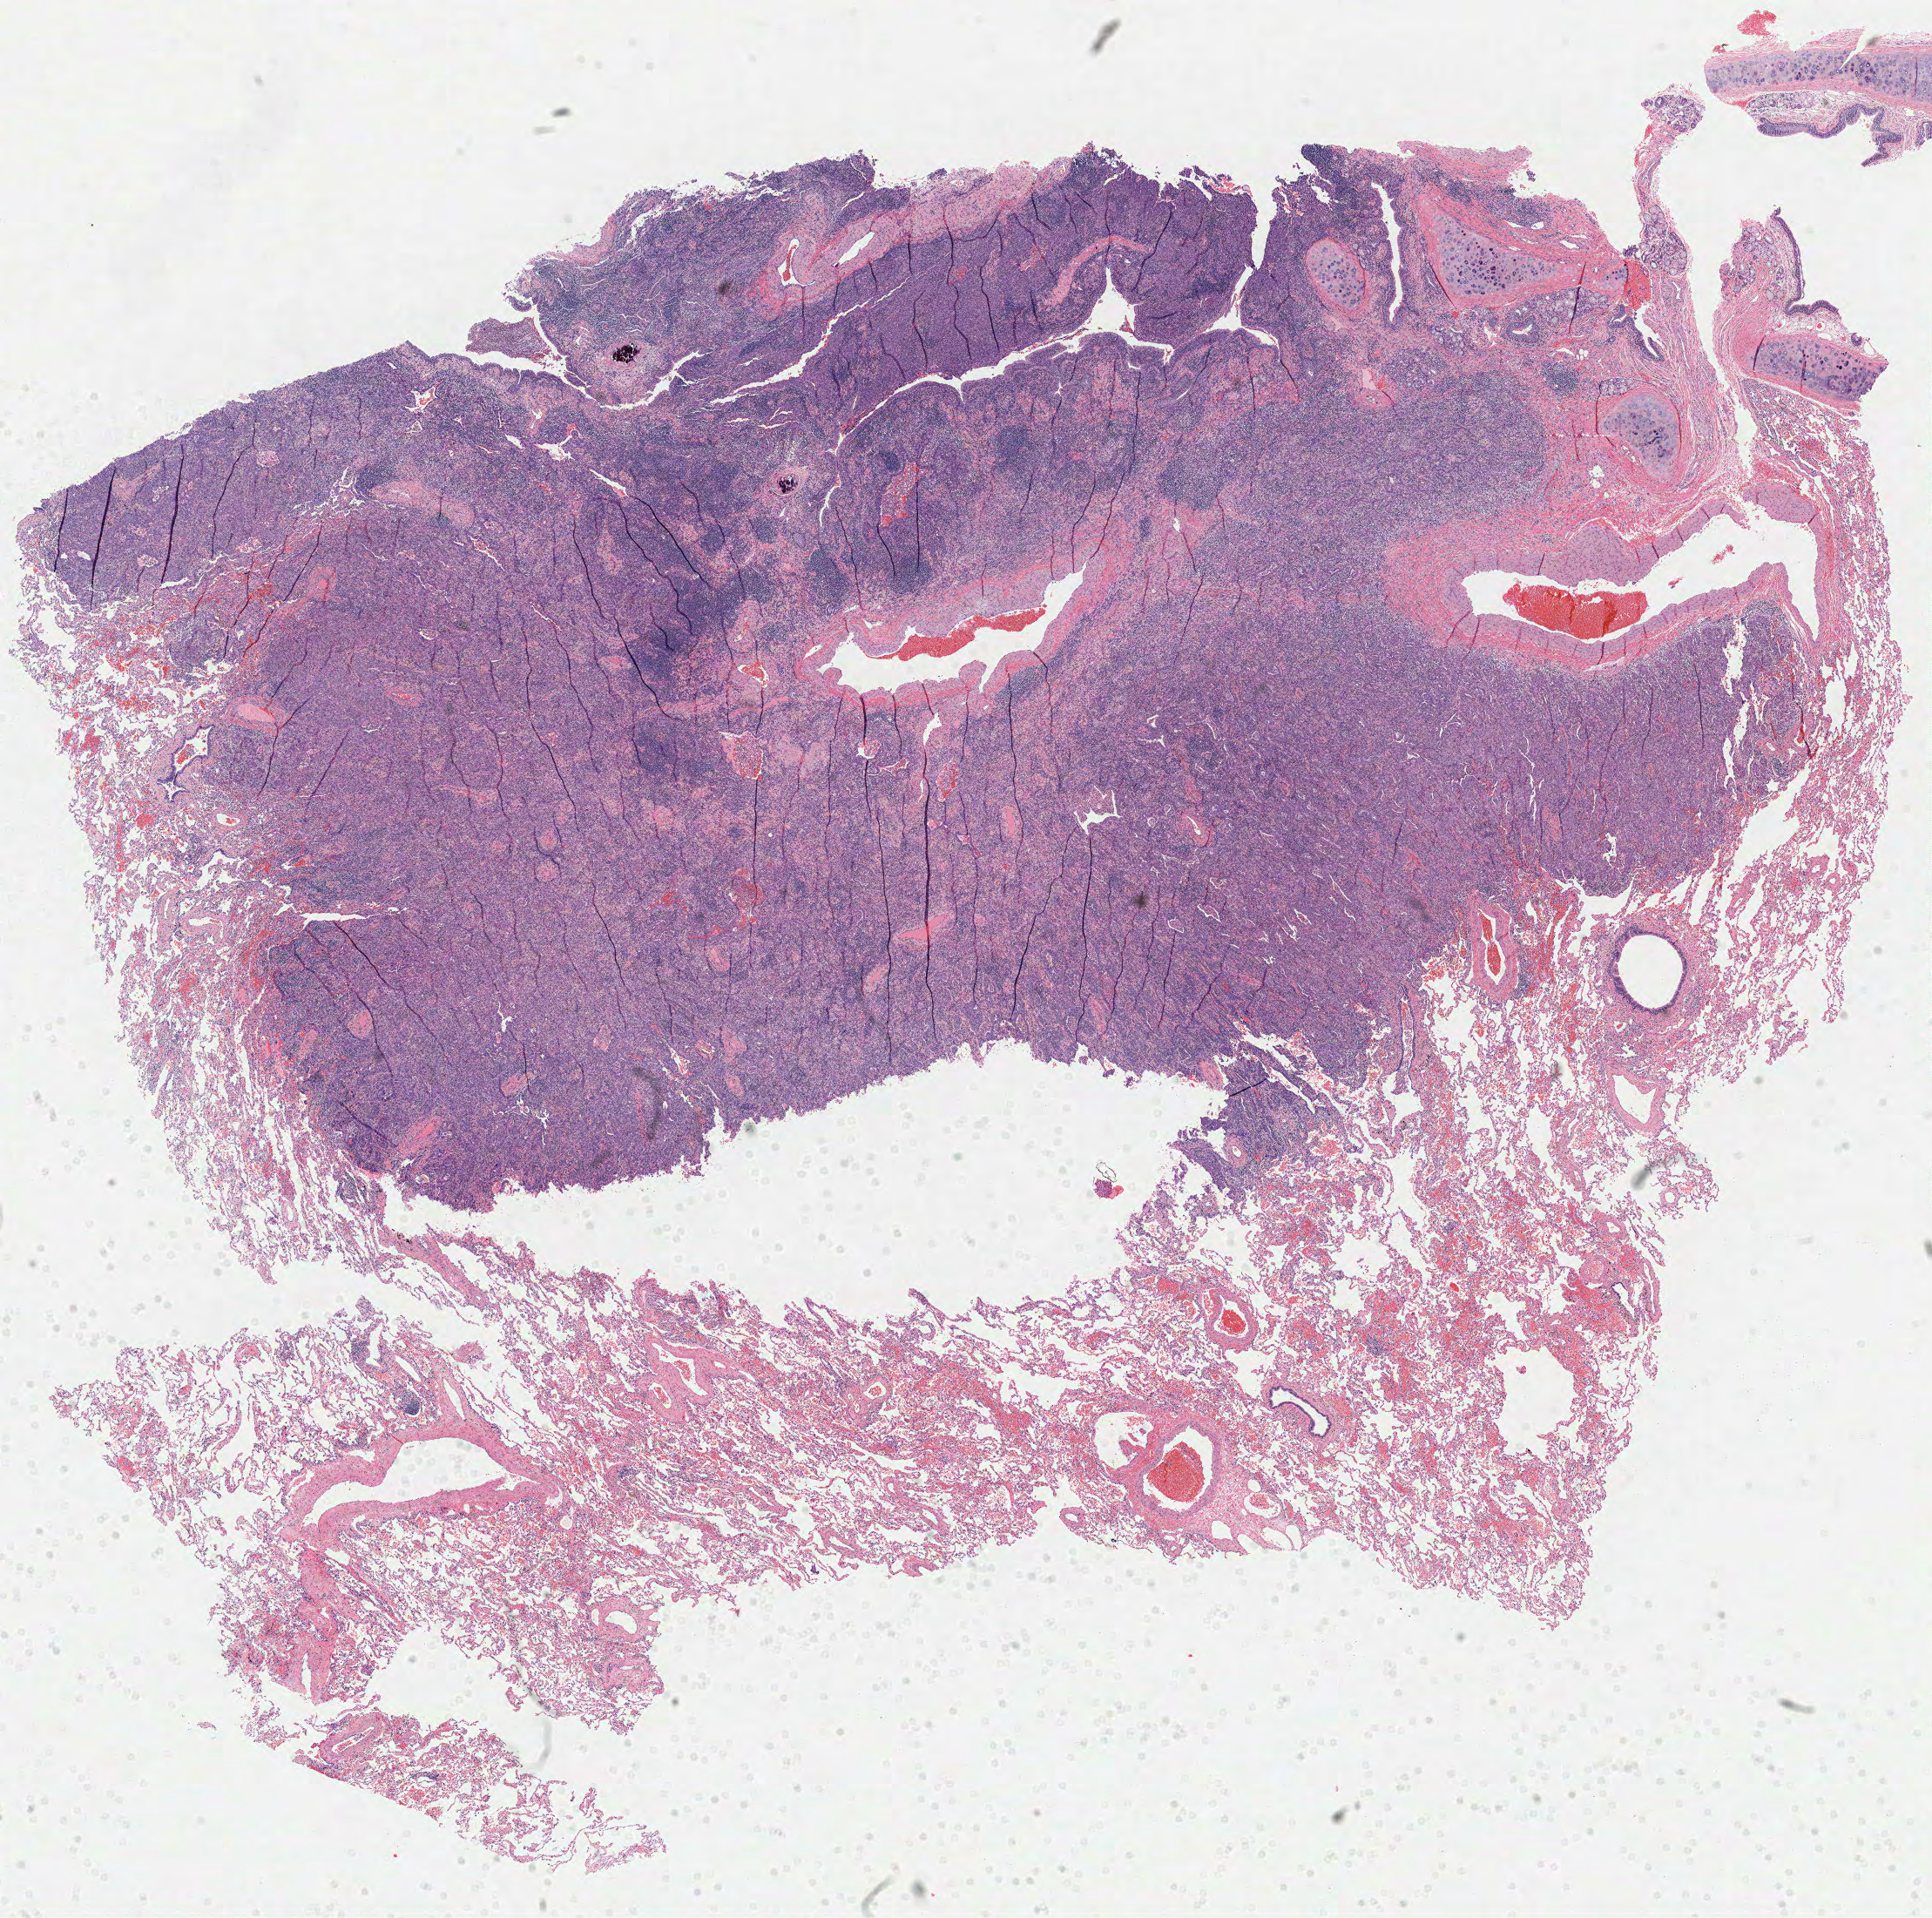
Hematoxylin and eosin (H&E) stained whole-slide image — shown as a low-resolution overview of the whole scanned area (about 17.9 x 17.8 mm, acquisition: 40x scan), formalin-fixed paraffin-embedded (FFPE) diagnostic section, primary tumour sample from the lung. Patient: female, age at initial diagnosis 59 years.
* laterality: left
* histologic diagnosis: Adenocarcinoma, NOS (upper lobe, lung)
* AJCC pathologic stage: IA (6th edition)
* TNM: T1 N0 M0